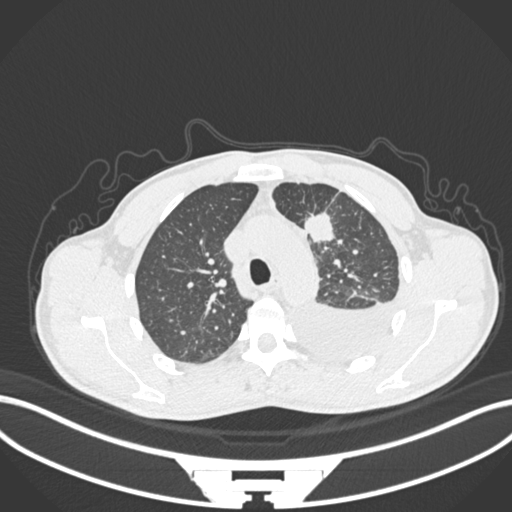
Chest CT, one axial slice. Position 161 of 244 along the scan axis. Lung window (W 1500 / L -600 HU). 512 × 512 image matrix, field of view 400 × 400 mm. Male patient, age 49 years. From the clinical record (not read from this slice): clinical TNM (as recorded): T1c N1 M1.
Annotated regions visible in this slice (bounding box drawn by a radiologist):
- lung tumour (recorded histology: adenocarcinoma): bounding box (x1, y1, x2, y2) in pixels: (304, 213, 336, 243)